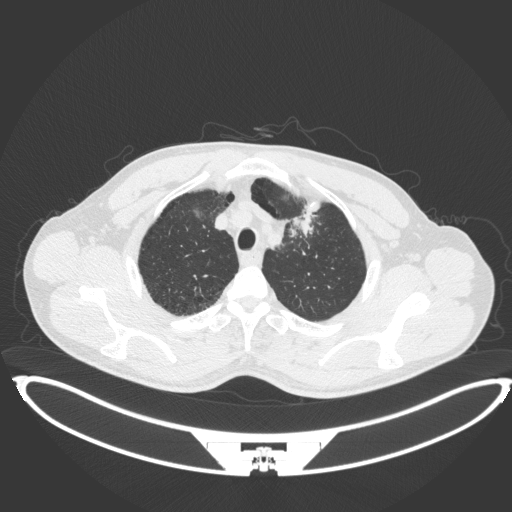
Chest CT, one axial slice; position 368 of 407 along the scan axis; reconstruction kernel B31f; lung window (W 1500 / L -600 HU); 1 mm slice thickness; 512 × 512 image matrix. Male patient, age 60 years. Case-level facts recorded for this patient, not image findings: clinical TNM (as recorded): T2a N0 M0.
Annotated regions visible in this slice (bounding box drawn by a radiologist):
- lung tumour (recorded histology: squamous cell carcinoma): bounding box (x1, y1, x2, y2) in pixels: (286, 206, 317, 241)